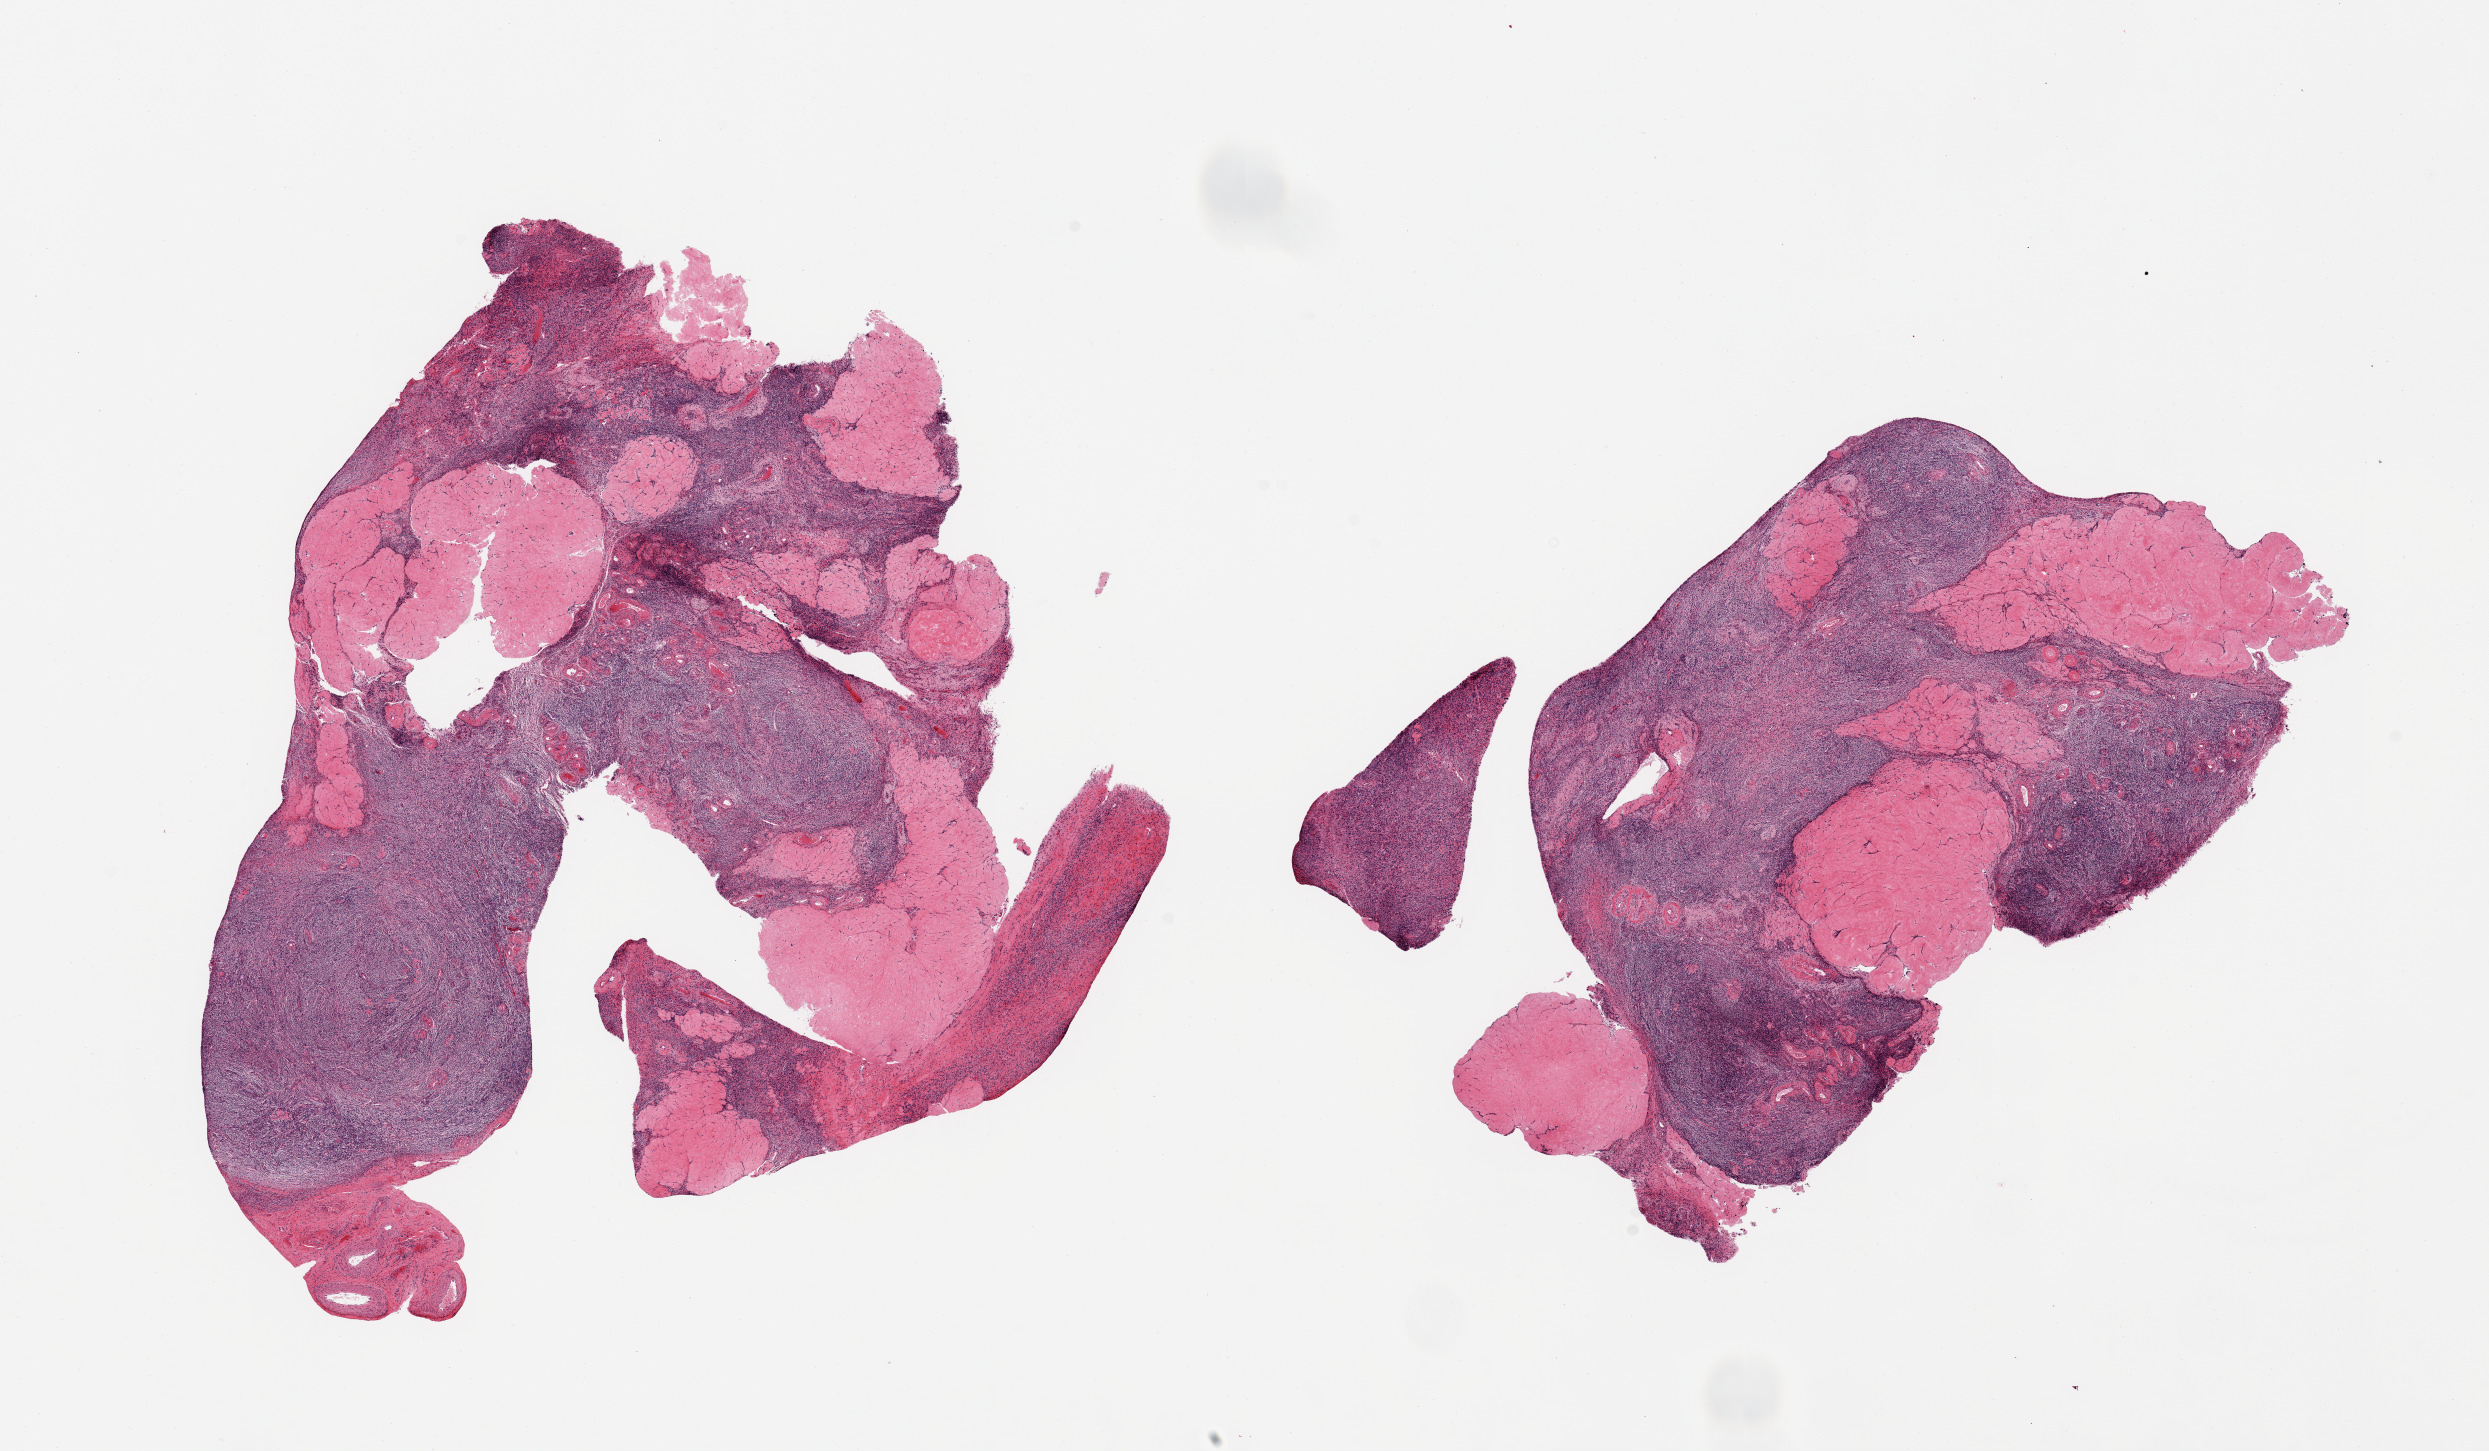
Digitized H&E-stained section, brightfield — whole scanned area (about 19.7 x 11.5 mm, from a 20x scan) shown as a low-resolution overview; PAXgene-fixed paraffin-embedded (PFPE) section; target tissue: ovary; donor tissue sample. Donor sex: female.
Review note (as recorded): 2 pieces; numerous corpora albicantia, 40% of area.